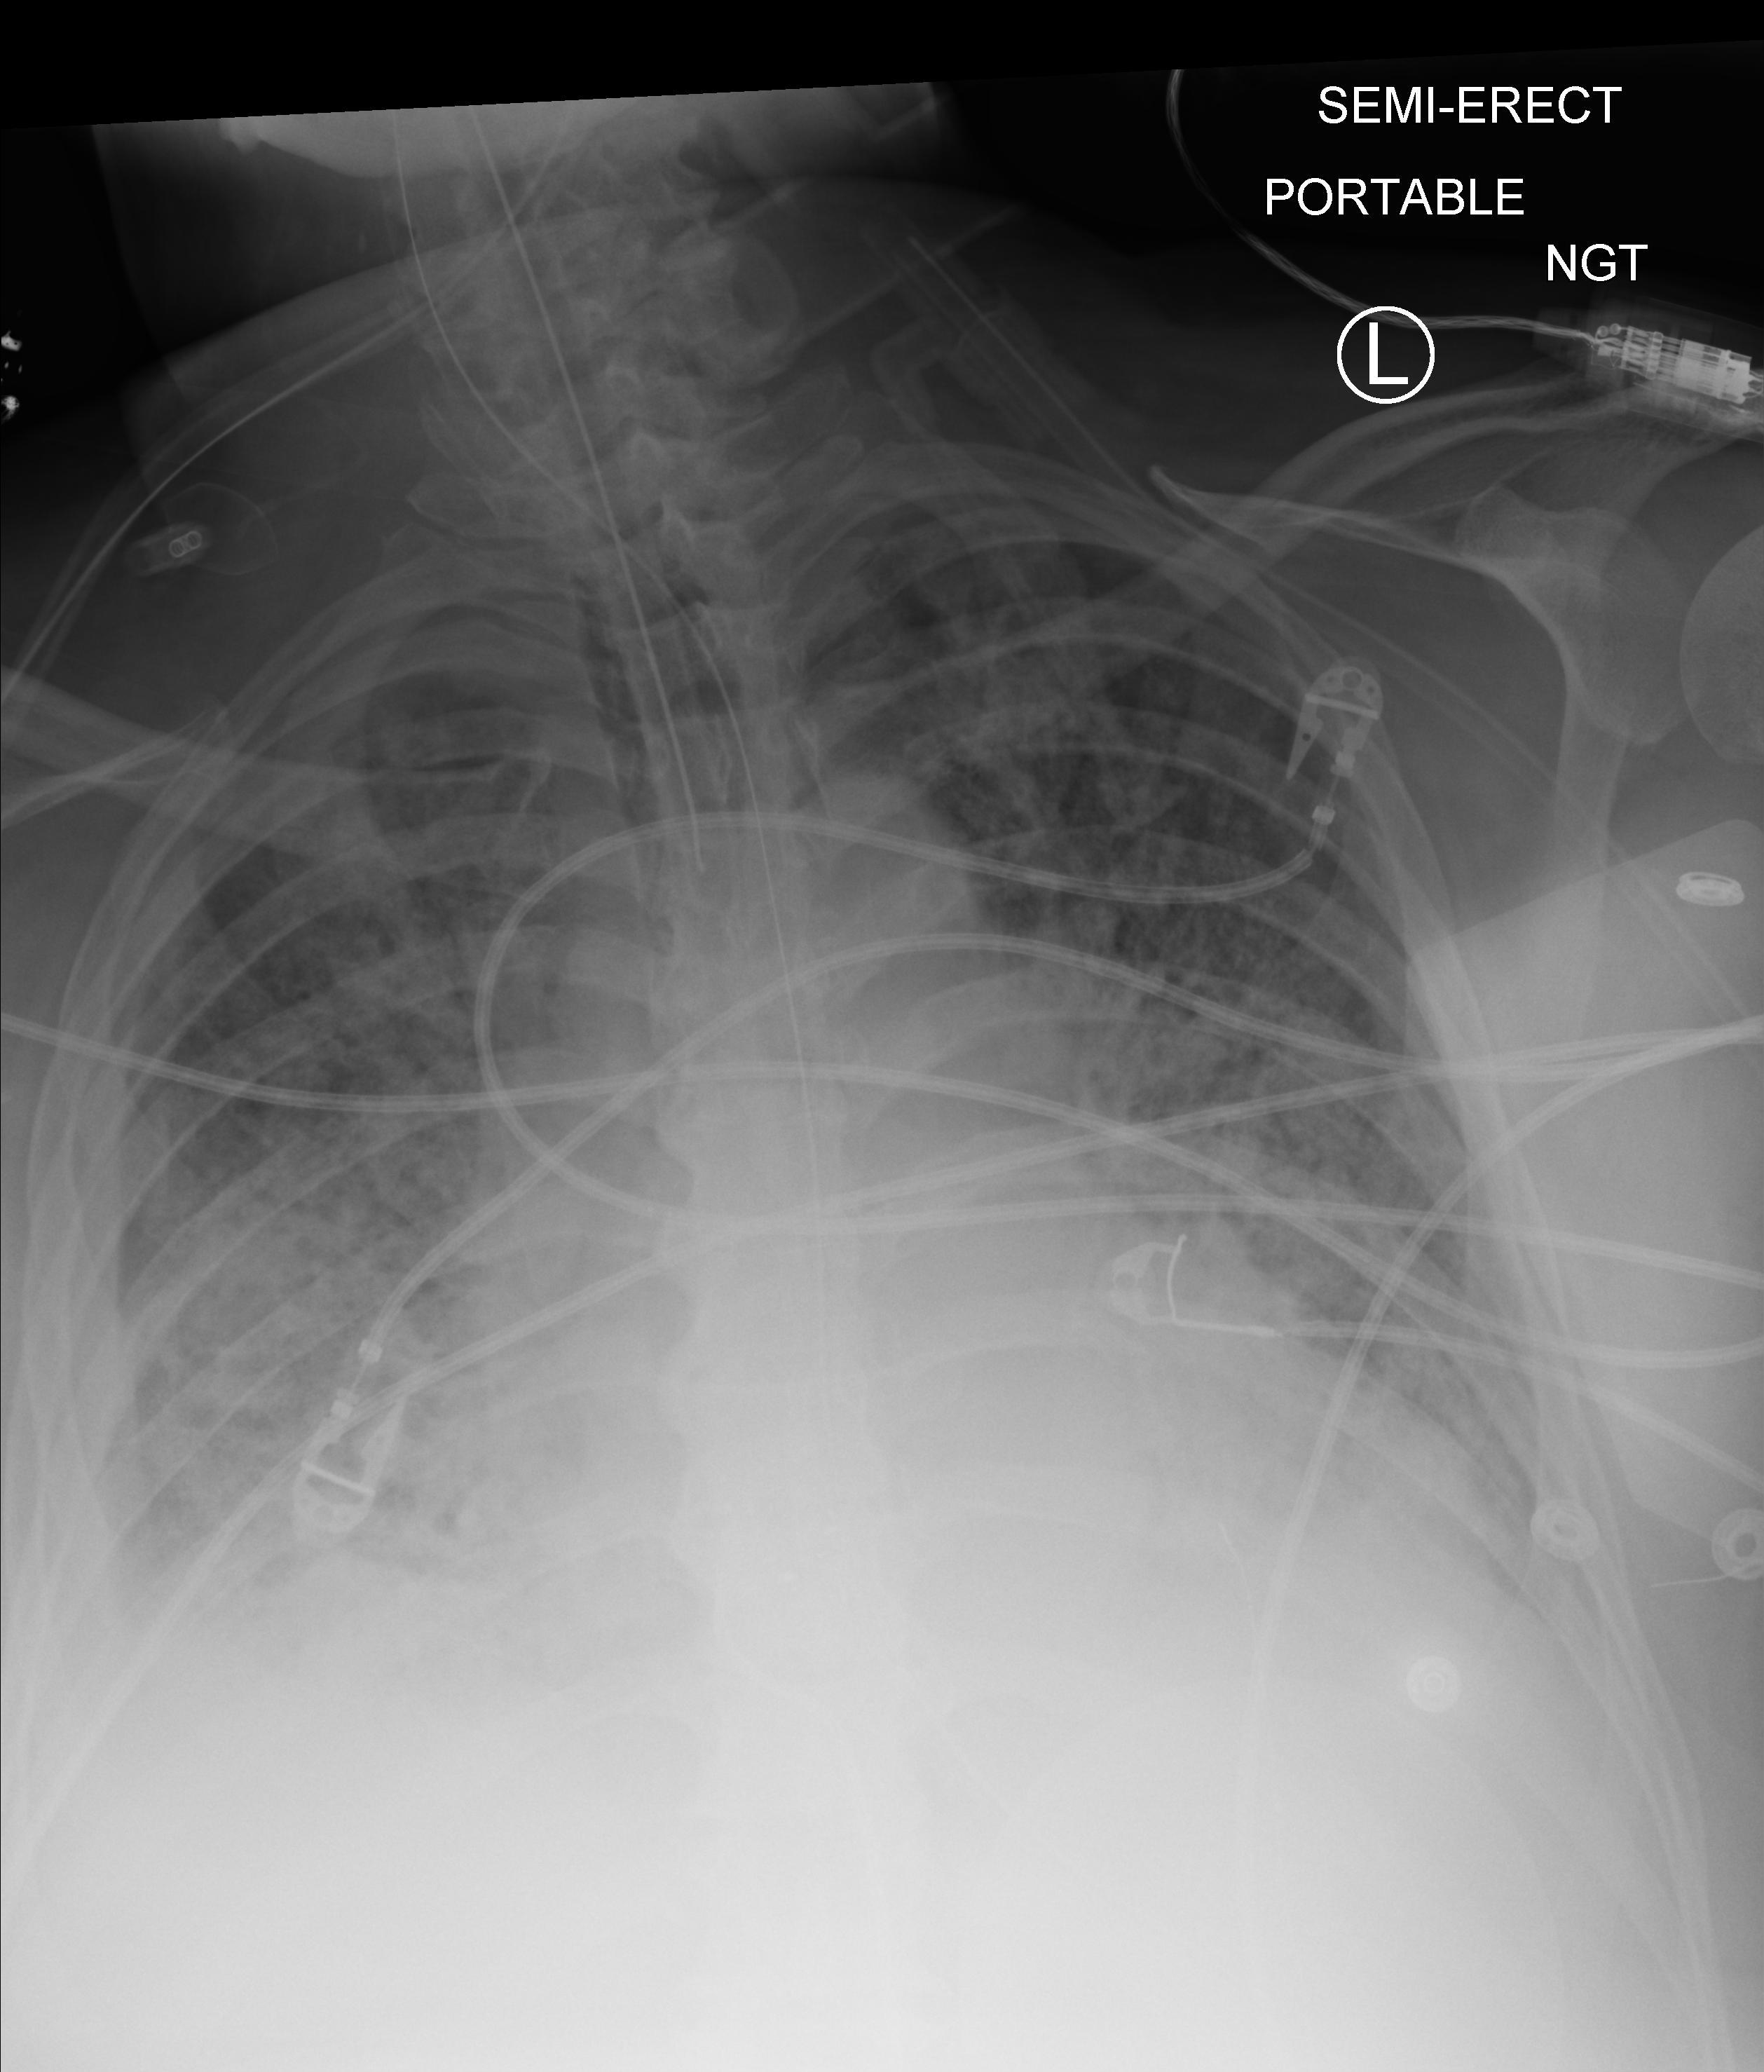
Chest X-ray (portable); anteroposterior (AP) projection. Patient hospitalised with COVID-19; male, aged 60–74 years.
From the hospital-stay record, not from the radiograph (when in the stay this image was taken is not recorded):
- admitted to intensive care during this hospital stay: yes
- smoking status (admission record): former
- mechanically ventilated during this hospital stay: yes